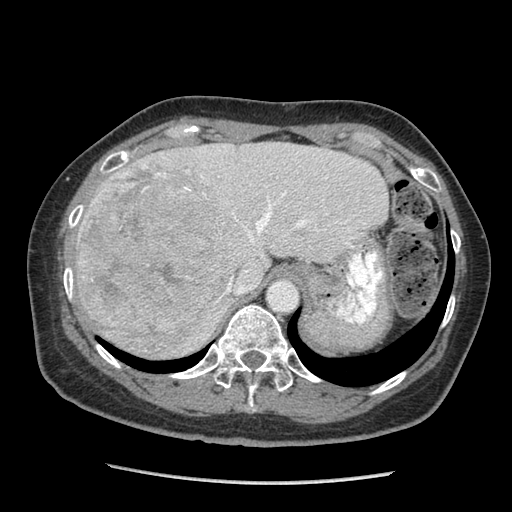
Contrast-enhanced abdominal CT (liver protocol), one axial slice. Slice 67 of 105 in the series (ordered by position). Reconstruction kernel STANDARD. 140 kVp. Soft-tissue window (W 400 / L 40 HU). 2.5 mm slice thickness. 512 × 512 image matrix, field of view 340 × 340 mm. Case-level facts recorded for this patient, not image findings: diagnosis: hepatocellular carcinoma (patient treated with transarterial chemoembolisation; whether this scan precedes or follows treatment is not stated here); TNM stage (as recorded): Stage-I; Child-Pugh class: A; tumour differentiation: moderately differentiated.
Outlined on this slice (semi-automatic segmentation, software-assisted and operator-edited):
- abdominal aorta: bounding box <268,280,298,311> (left, top, right, bottom; pixels)
- liver parenchyma outside the tumour (the mass and vessels are separate outlines, so this box may not span the whole liver): <74,142,388,358>
- mass: <74,157,228,355>
- liver vessels: <114,165,349,294>